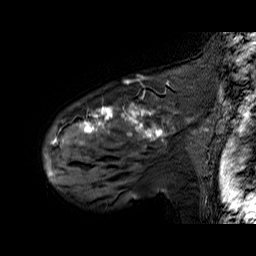
Breast MRI (dynamic contrast-enhanced), one sagittal slice; dynamic contrast-enhanced series, time point 2 of 6 at this slice position (early post-contrast); 1.5 T; TE 6.3 ms, TR 32.9 ms; 256 × 256 image matrix, field of view 200 × 200 mm. Female patient. Case-level facts recorded for this patient, not image findings: setting: breast cancer imaged before/during neoadjuvant chemotherapy; receptor status: HER2-positive.
Outlined on this slice (semi-automatically segmented with operator editing):
- analysis volume of interest (the breast-tissue region the enhancement analysis was run in; not a lesion): bounding box (x1, y1, x2, y2) in pixels: (48, 92, 195, 174)
- tumour enhancement mask (voxels above the 100 % enhancement threshold inside the analysis volume of interest): (52, 106, 164, 144)